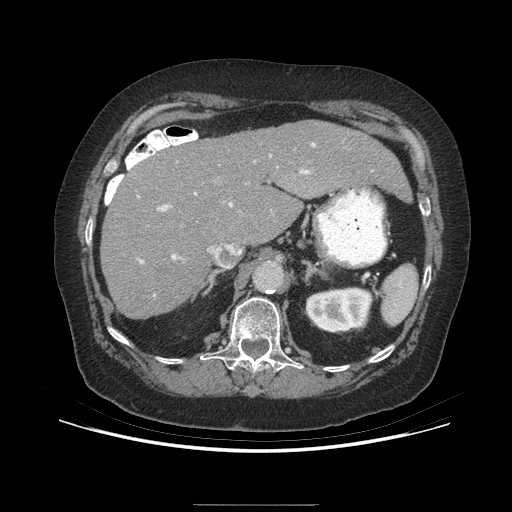
Contrast-enhanced abdominal CT (liver protocol), one axial slice; position 160 of 192 along the scan axis; soft-tissue window (W 400 / L 40 HU); 2.5 mm slice thickness; 512 × 512 image matrix. Case-level facts recorded for this patient, not image findings: diagnosis: hepatocellular carcinoma (patient treated with transarterial chemoembolisation; whether this scan precedes or follows treatment is not stated here); TNM stage (as recorded): Stage-I; Child-Pugh class: A; tumour nodularity: uninodular; tumour size: 3.2 cm.
Annotated regions visible in this slice (semi-automatic segmentation, software-assisted and operator-edited):
- liver parenchyma outside the tumour (the mass and vessels are separate outlines, so this box may not span the whole liver): bounding box (x1, y1, x2, y2) in pixels: (100, 121, 408, 318)
- liver vessels: (138, 143, 316, 264)